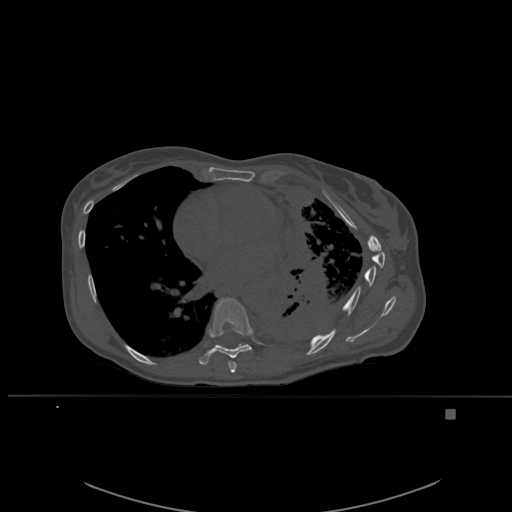
CT including the spine, one axial slice; position 349 of 537 along the scan axis; bone window (W 1800 / L 400 HU); 512 × 512 image matrix. Female patient, age 45 years. From the clinical record (not read from this slice): primary cancer: lung.
Outlined on this slice (semi-automatic segmentation, software-assisted and operator-edited):
- T7 vertebra: bounding box (x1, y1, x2, y2) in pixels: (228, 361, 237, 373)
- T8 vertebra: (198, 298, 252, 365)
- T9 vertebra: (216, 344, 248, 348)